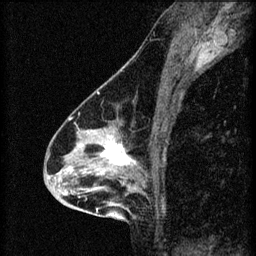
Breast MRI (dynamic contrast-enhanced), one sagittal slice. Slice 38 of 60 in the series (ordered by position). 3 images stored at this slice position (order not interpretable as contrast timing). 1.5 T. TE 4.2 ms, TR 8.2 ms. 2 mm slice thickness. 256 × 256 image matrix, field of view 180 × 180 mm. Female patient, age 46 years.
Structures marked on this image (semi-automatic segmentation, software-assisted and operator-edited):
- analysis volume of interest (the breast-tissue region the enhancement analysis was run in; not a lesion): box from (x=55, y=114) to (x=148, y=209) px
- tumour enhancement mask (voxels above the 70 % enhancement threshold inside the analysis volume of interest): (x=65, y=118)–(x=137, y=197)